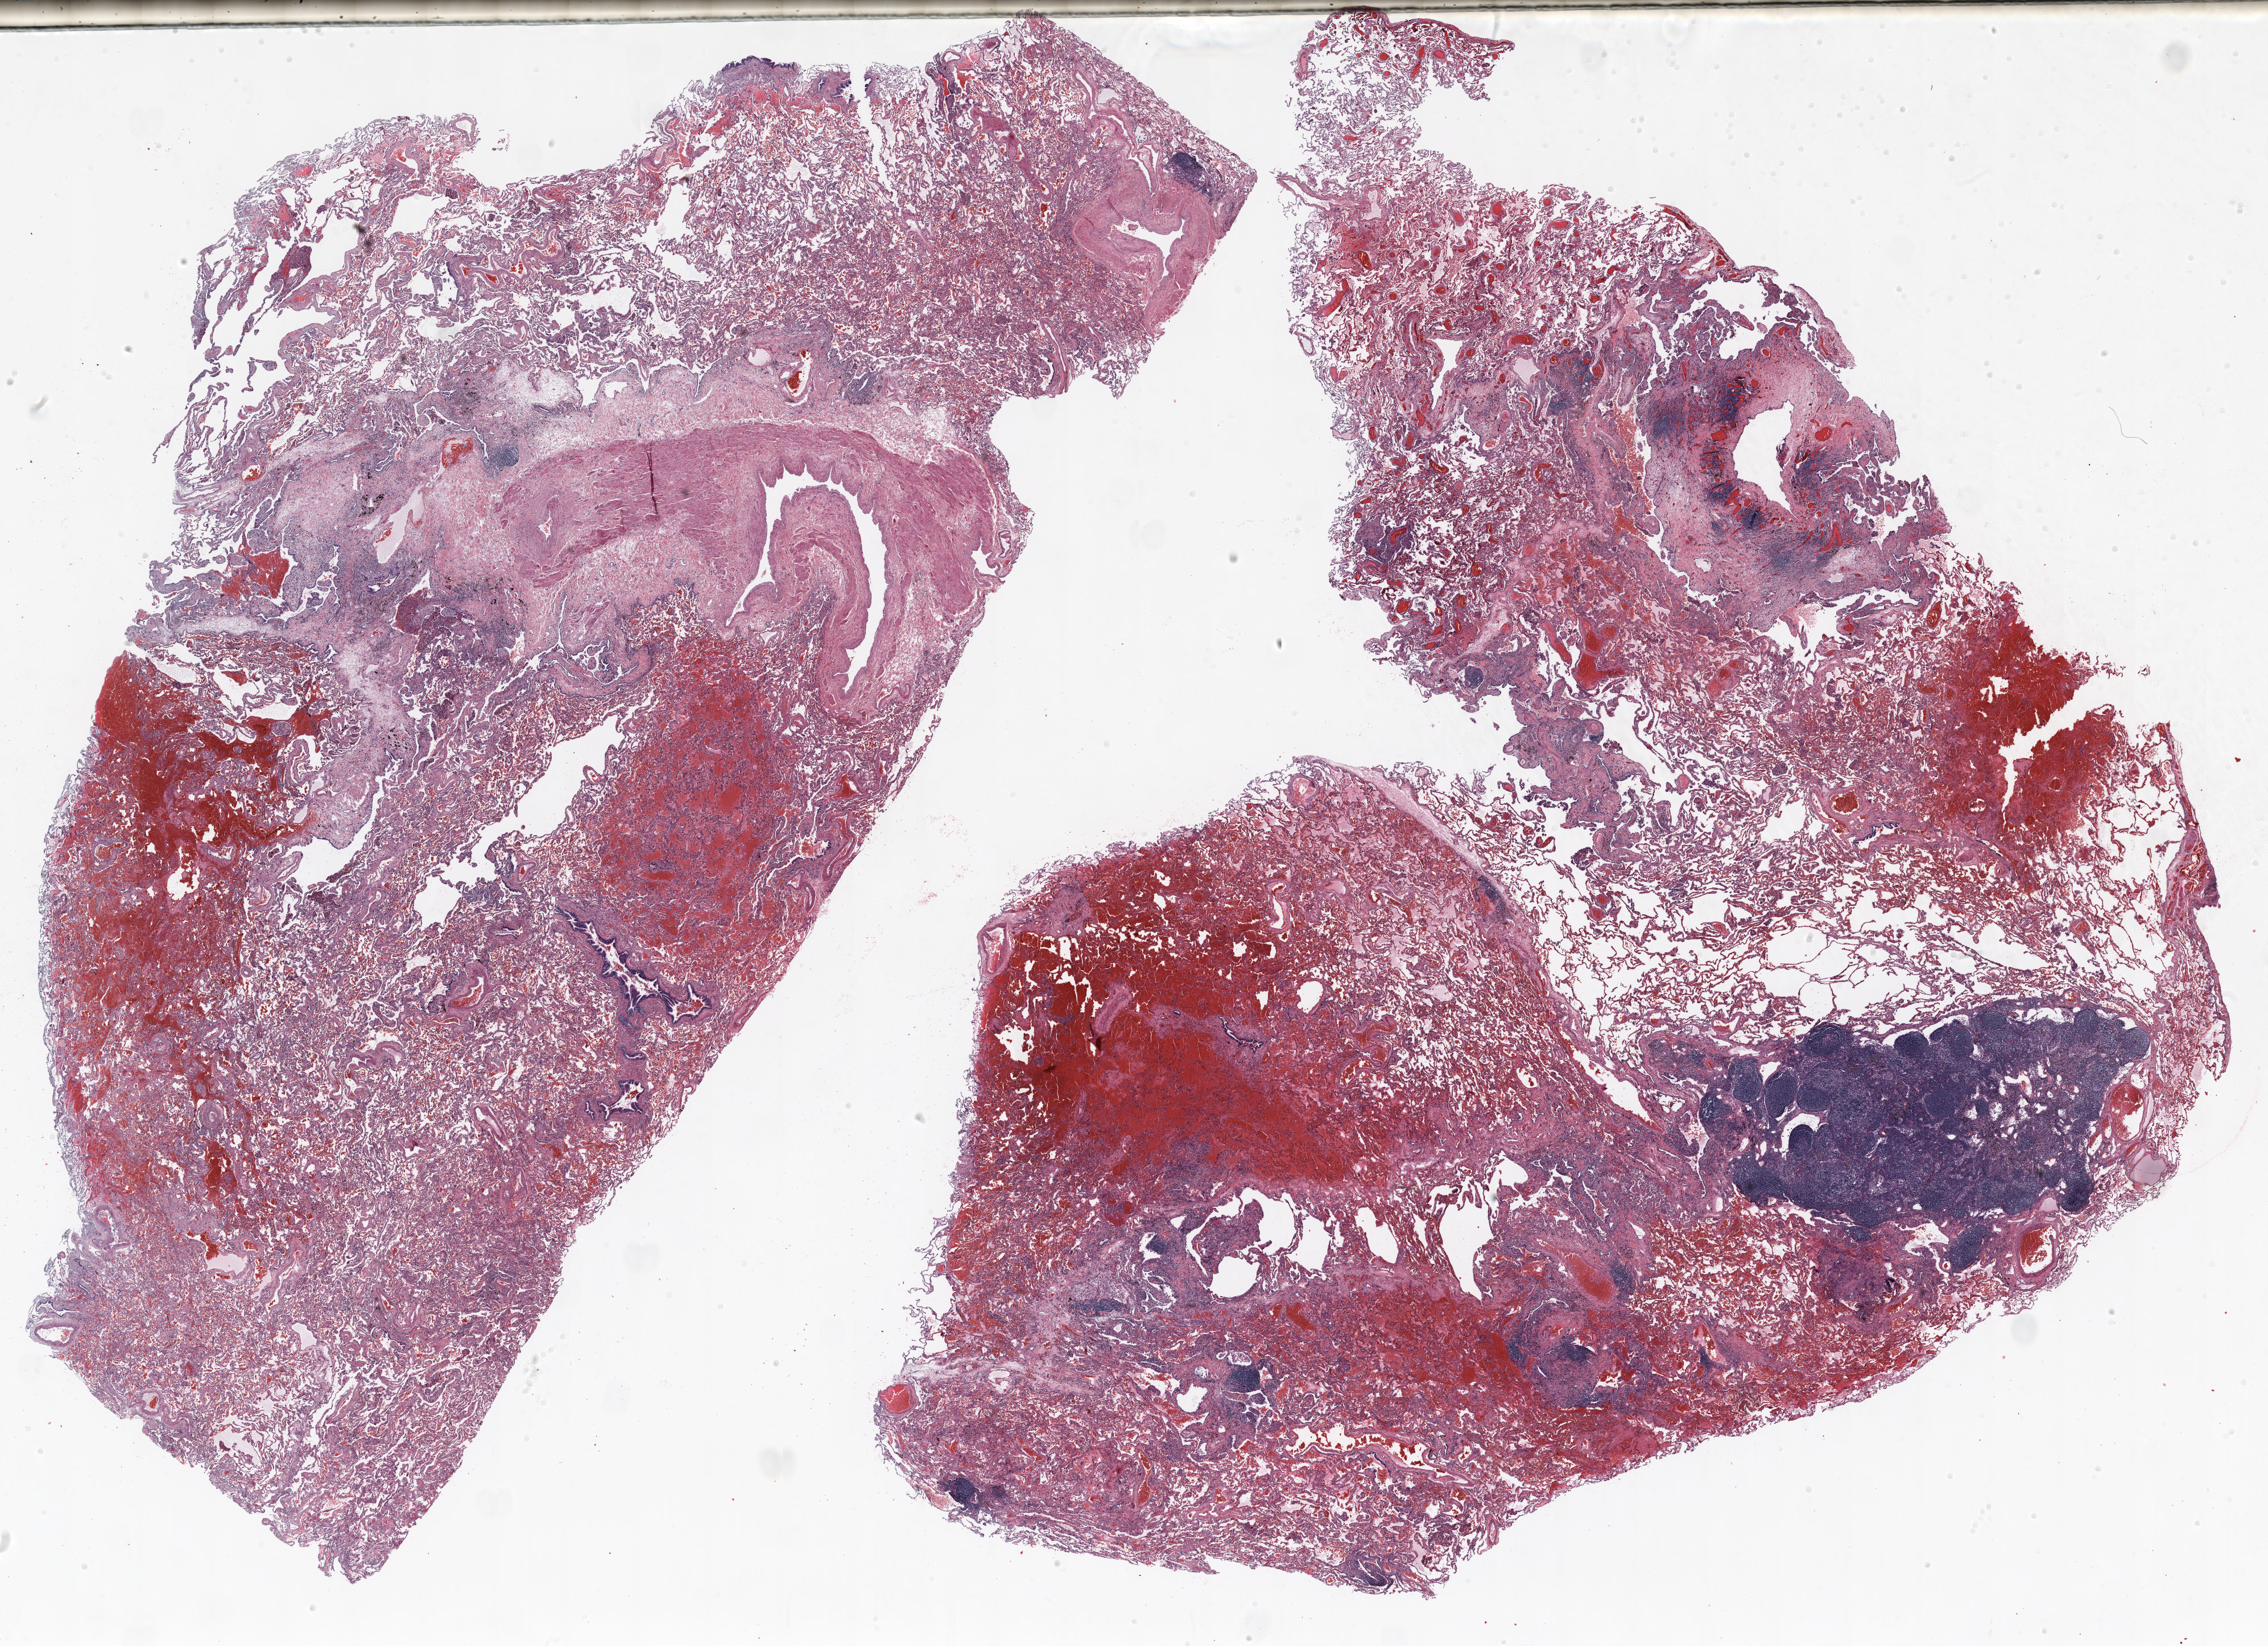
Whole-slide histology image, H&E-stained, shown as a low-resolution overview of the whole scanned area (about 32.0 x 23.2 mm, slide scanned at 20x). Formalin-fixed paraffin-embedded (FFPE) section. Lung. Male patient, aged 62 at enrolment. Current smoker at enrolment. Grade: moderately differentiated (G2).
Tumour size (pathology): 16 mm. Participant's lung-cancer diagnosis: Adenocarcinoma, NOS (ICD-O-3 8140/3). Primary tumour location (clinical record): right upper lobe. Stage (AJCC 6th edition): IA.